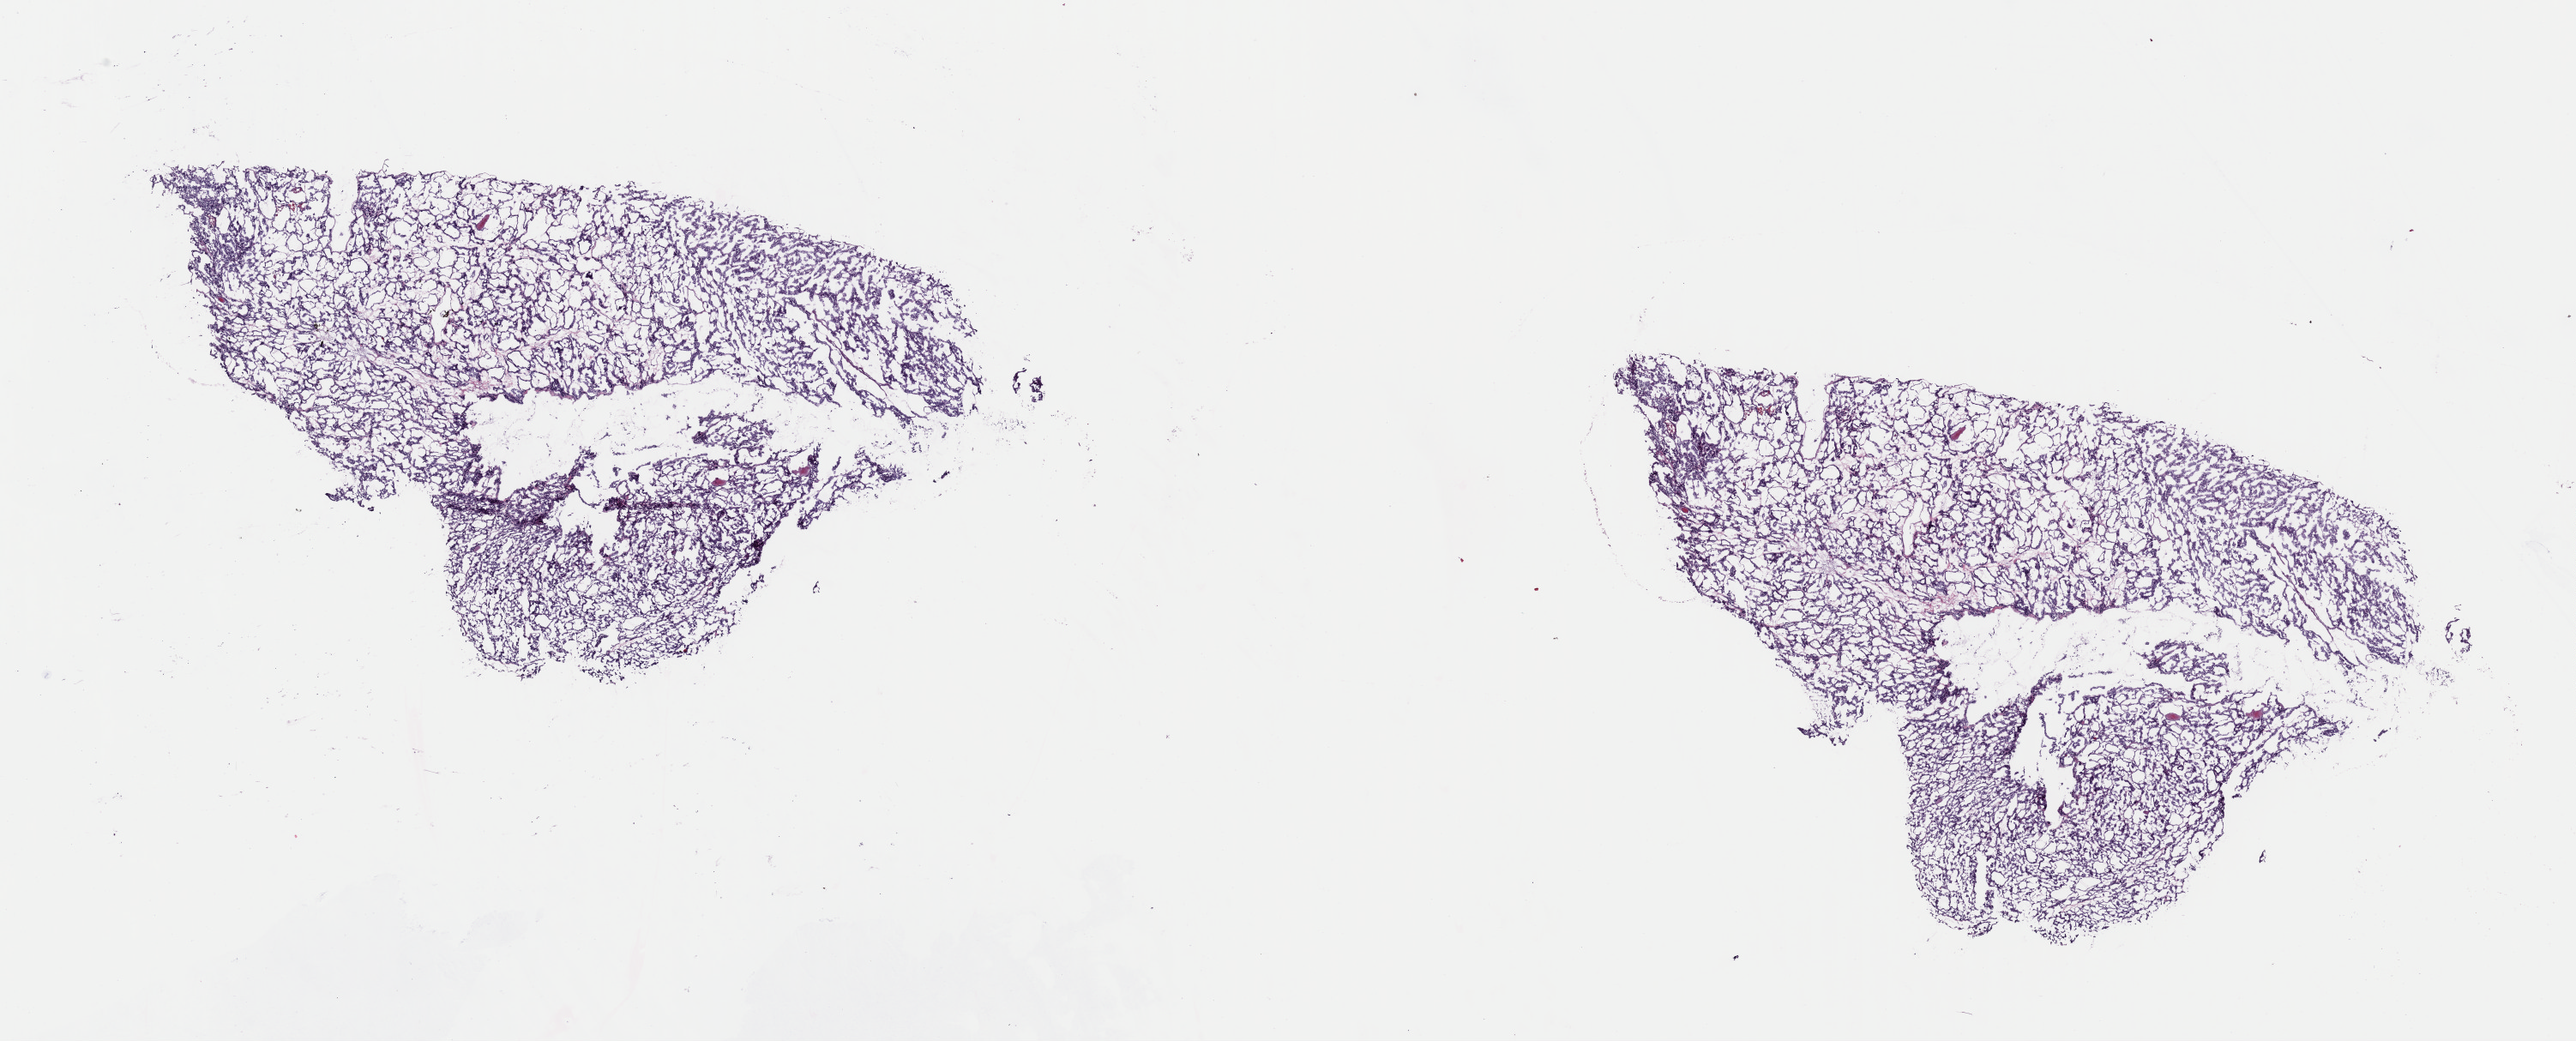
Whole-slide histology image, H&E-stained — shown as a low-resolution overview of the whole scanned area (about 23.7 x 9.6 mm, from a 40x scan). Frozen section from the top of the tissue portion. Sample: primary tumour, thyroid. Patient: female, age at initial diagnosis 41 years.
Diagnosis: Papillary adenocarcinoma, NOS (thyroid gland).